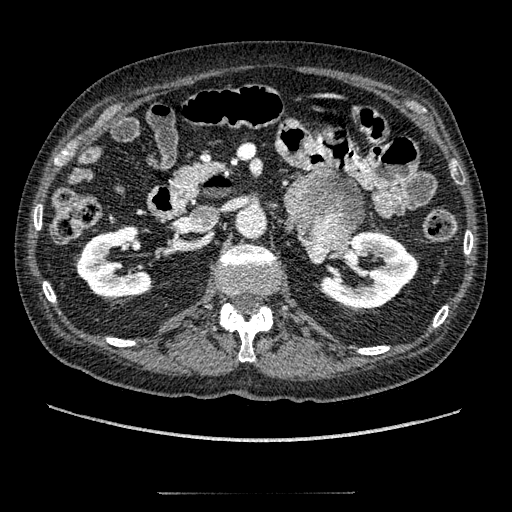
Contrast-enhanced abdominal CT, one axial slice; slice 99 of 274 in the series (ordered by position); reconstruction kernel STANDARD; 120 kVp; intravenous contrast given; soft-tissue window (W 400 / L 40 HU); 1.25 mm slice thickness; 512 × 512 image matrix. Male patient, age 69 years. Case-level facts recorded for this patient, not image findings: diagnosis: adrenocortical carcinoma; tumour side: left adrenal; tumour size at pathology: 6.1 cm; Ki-67 index: 10 %; stage (as recorded): 3.
Annotated regions visible in this slice (semi-automatic segmentation, software-assisted and operator-edited):
- mass: bounding box (x1, y1, x2, y2) in pixels: (287, 169, 362, 262)